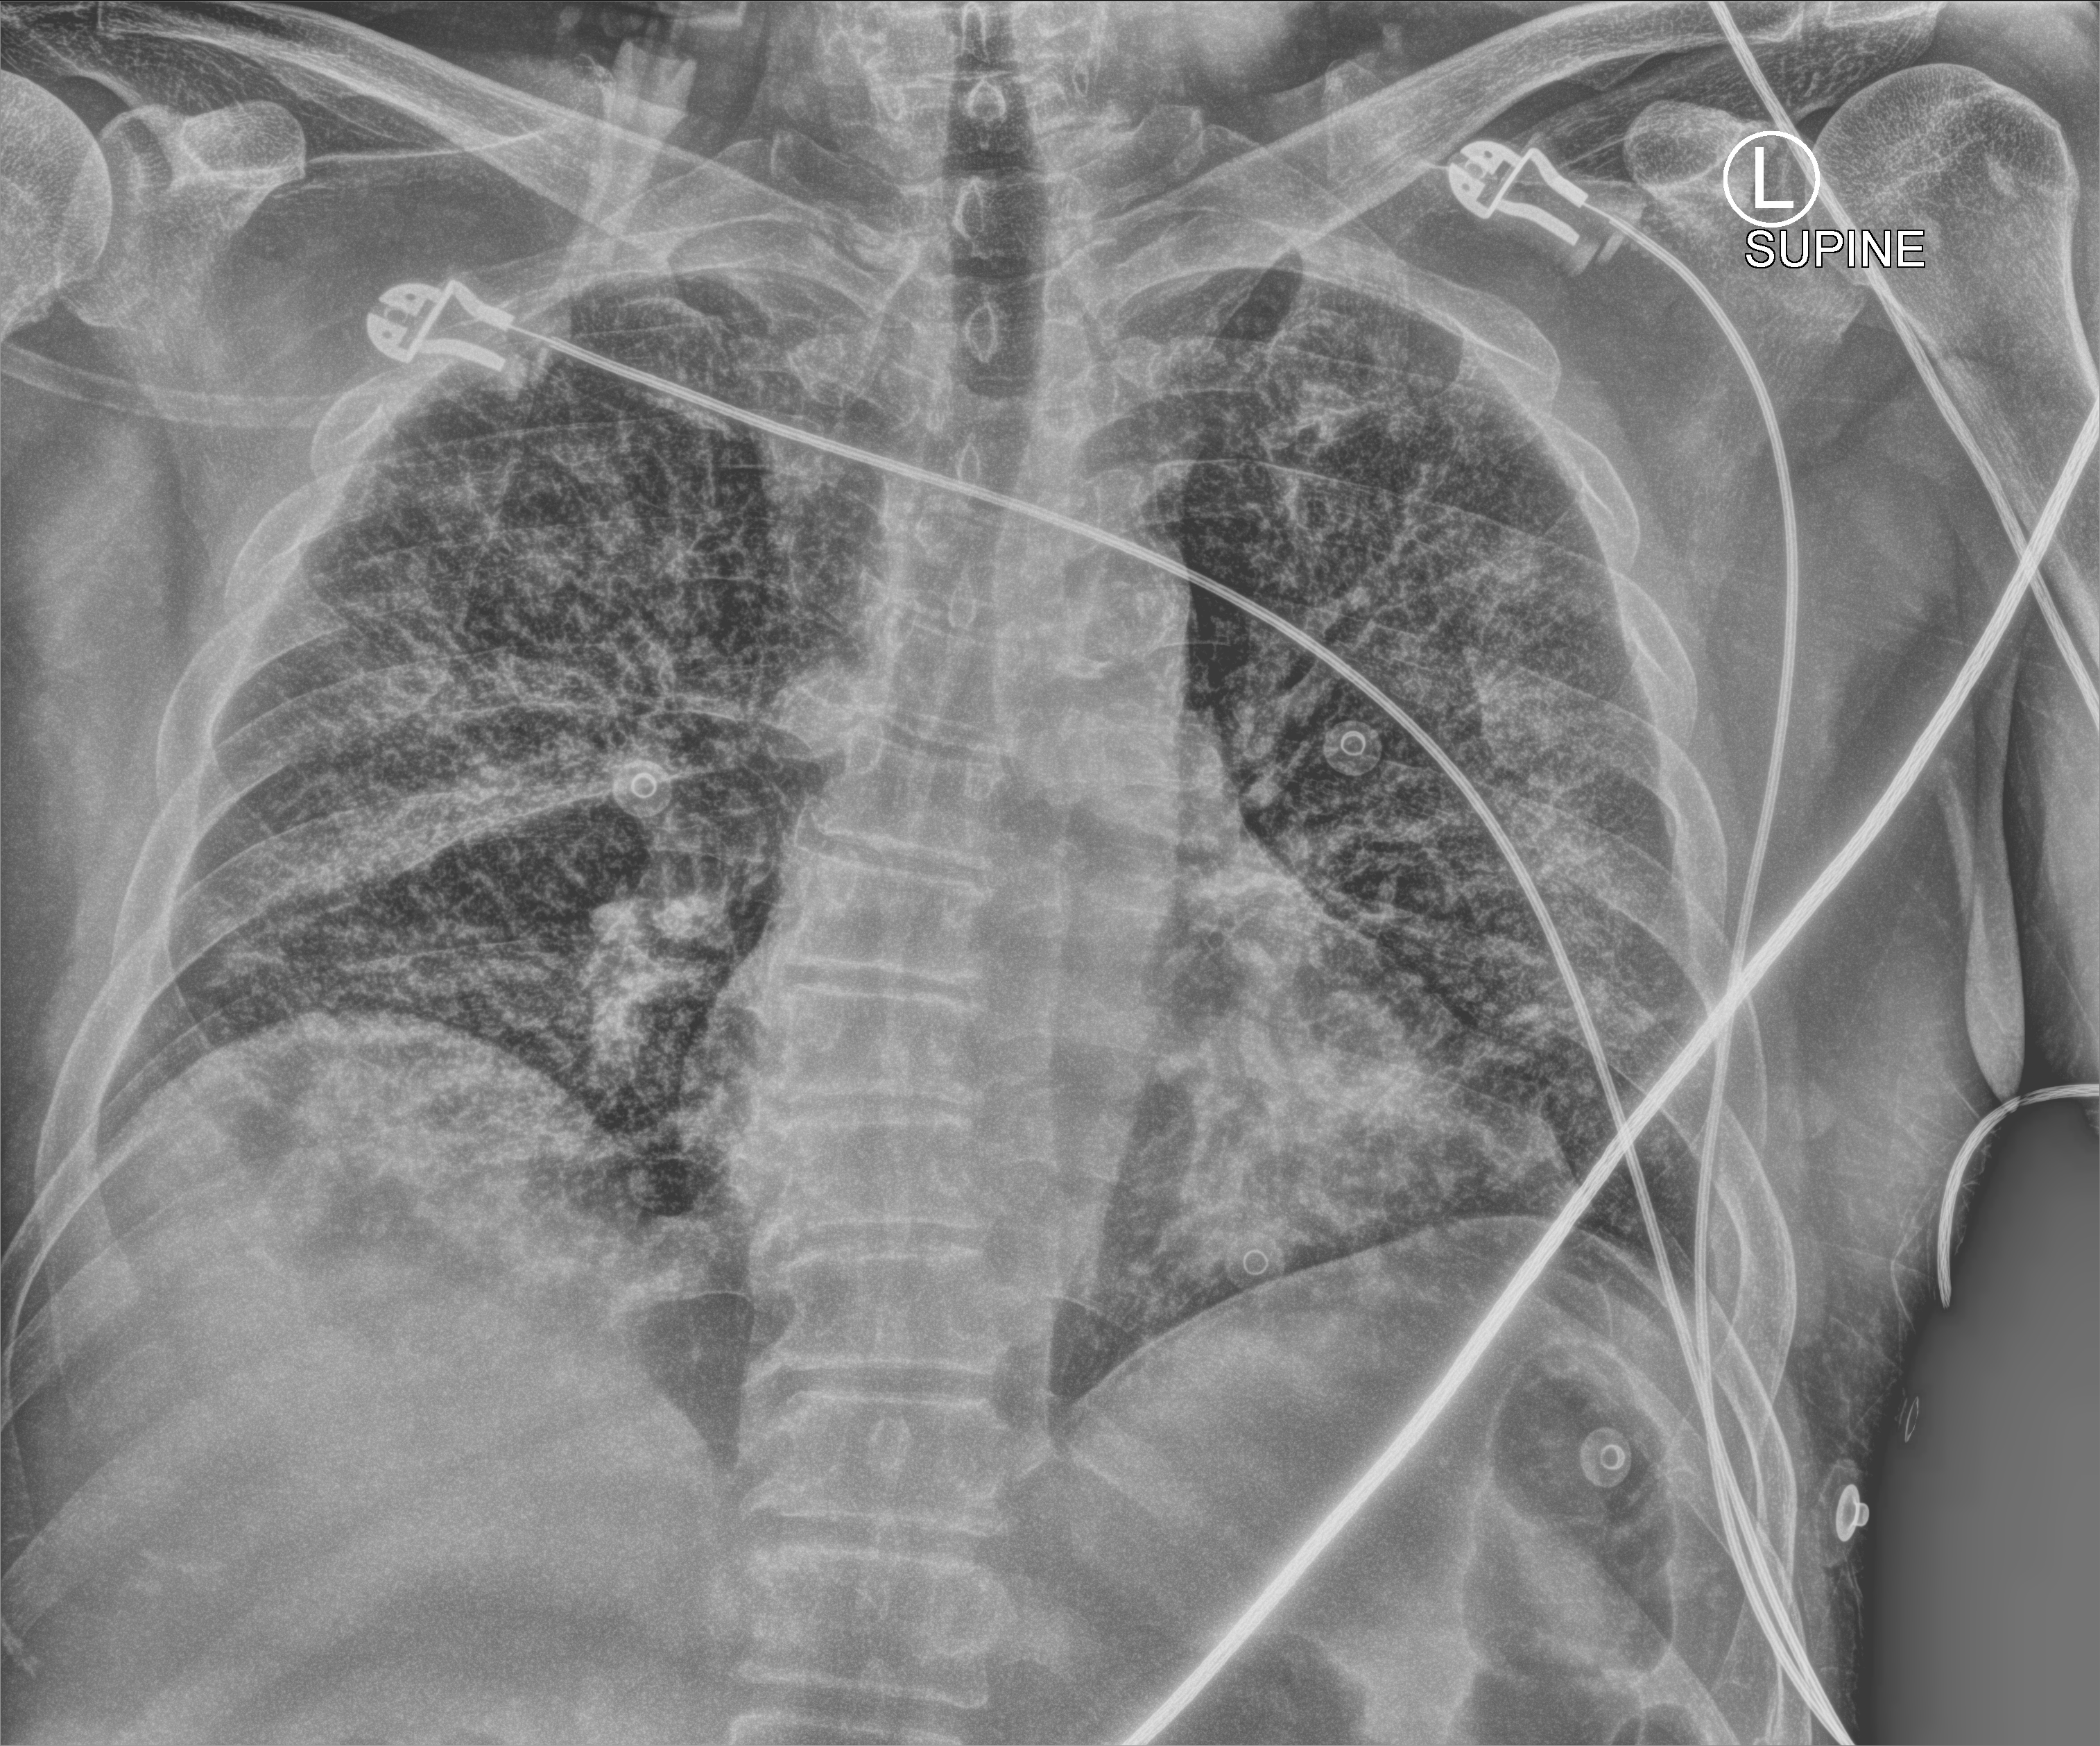
Chest X-ray (portable); anteroposterior (AP) projection. Male patient hospitalised with COVID-19, age 18–59 years.
Admission-level facts for this patient (not findings on this image; timing relative to this image not recorded):
- mechanically ventilated during this hospital stay: no